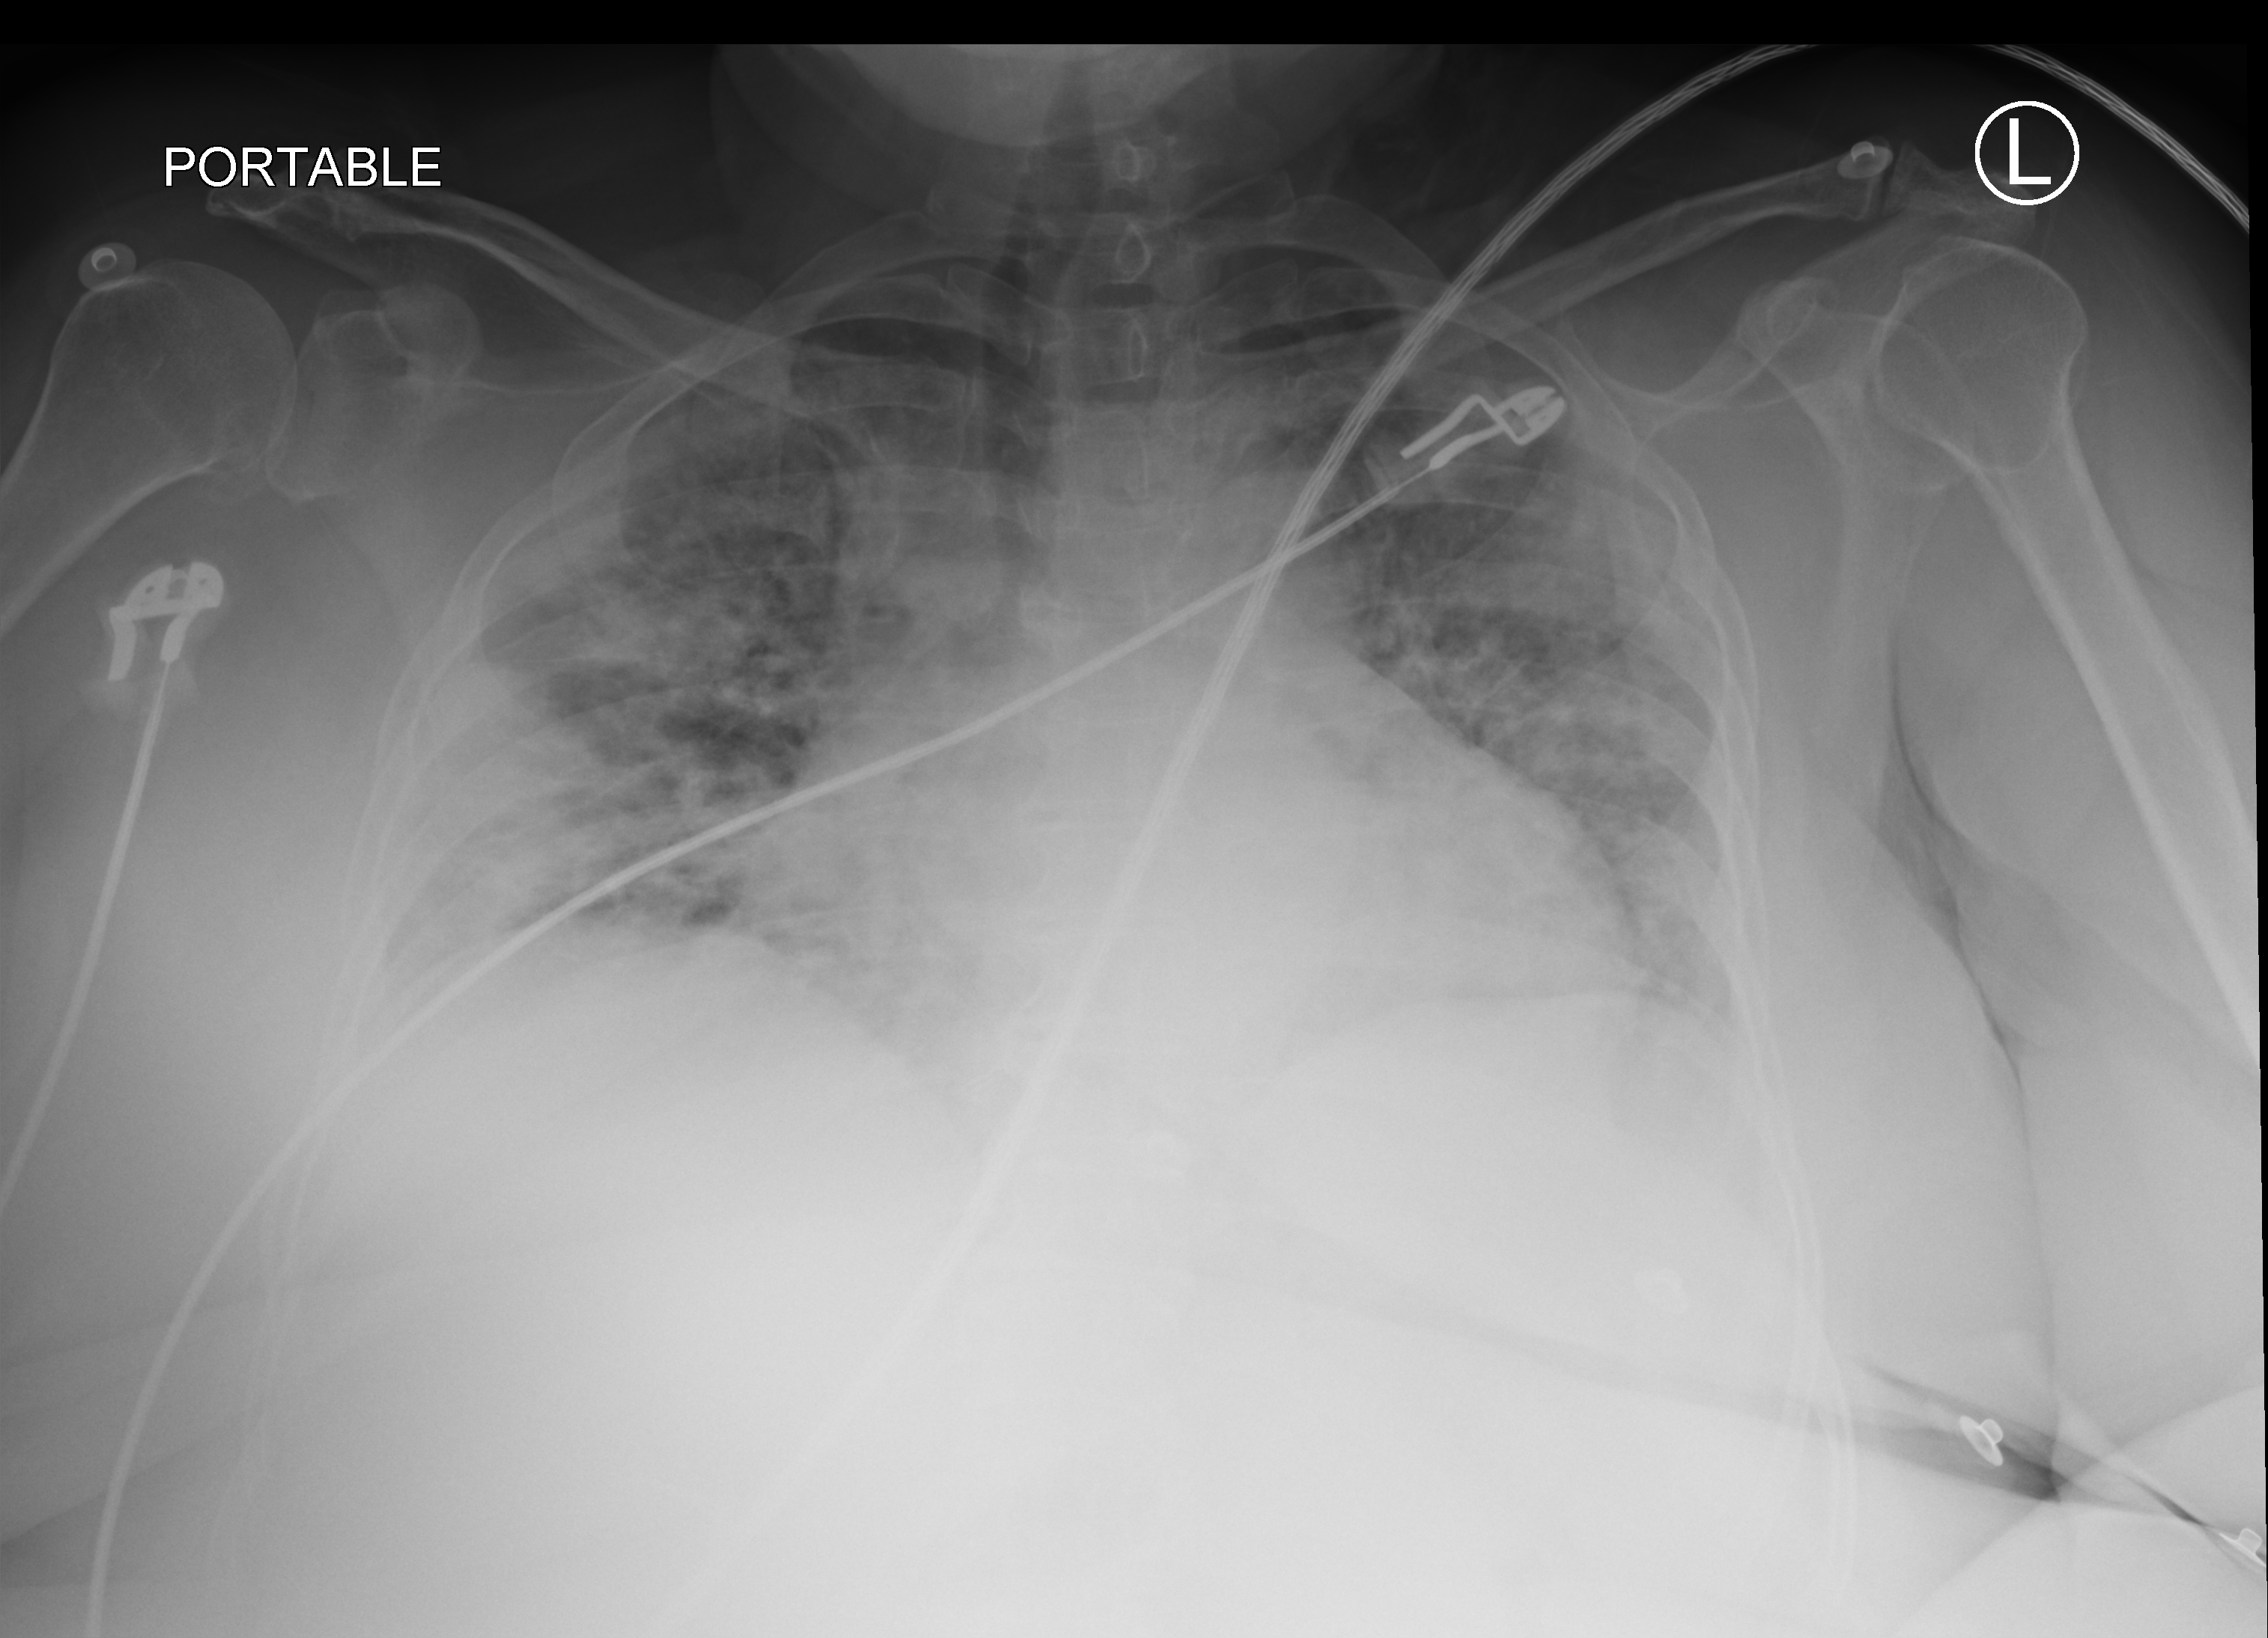
Bedside chest radiograph (computed radiography); anteroposterior (AP) projection. Female patient hospitalised with COVID-19, age 60–74 years.
Hospital-stay facts (about this admission, not read from this image; timing relative to this image not recorded):
- mechanically ventilated during this hospital stay: no